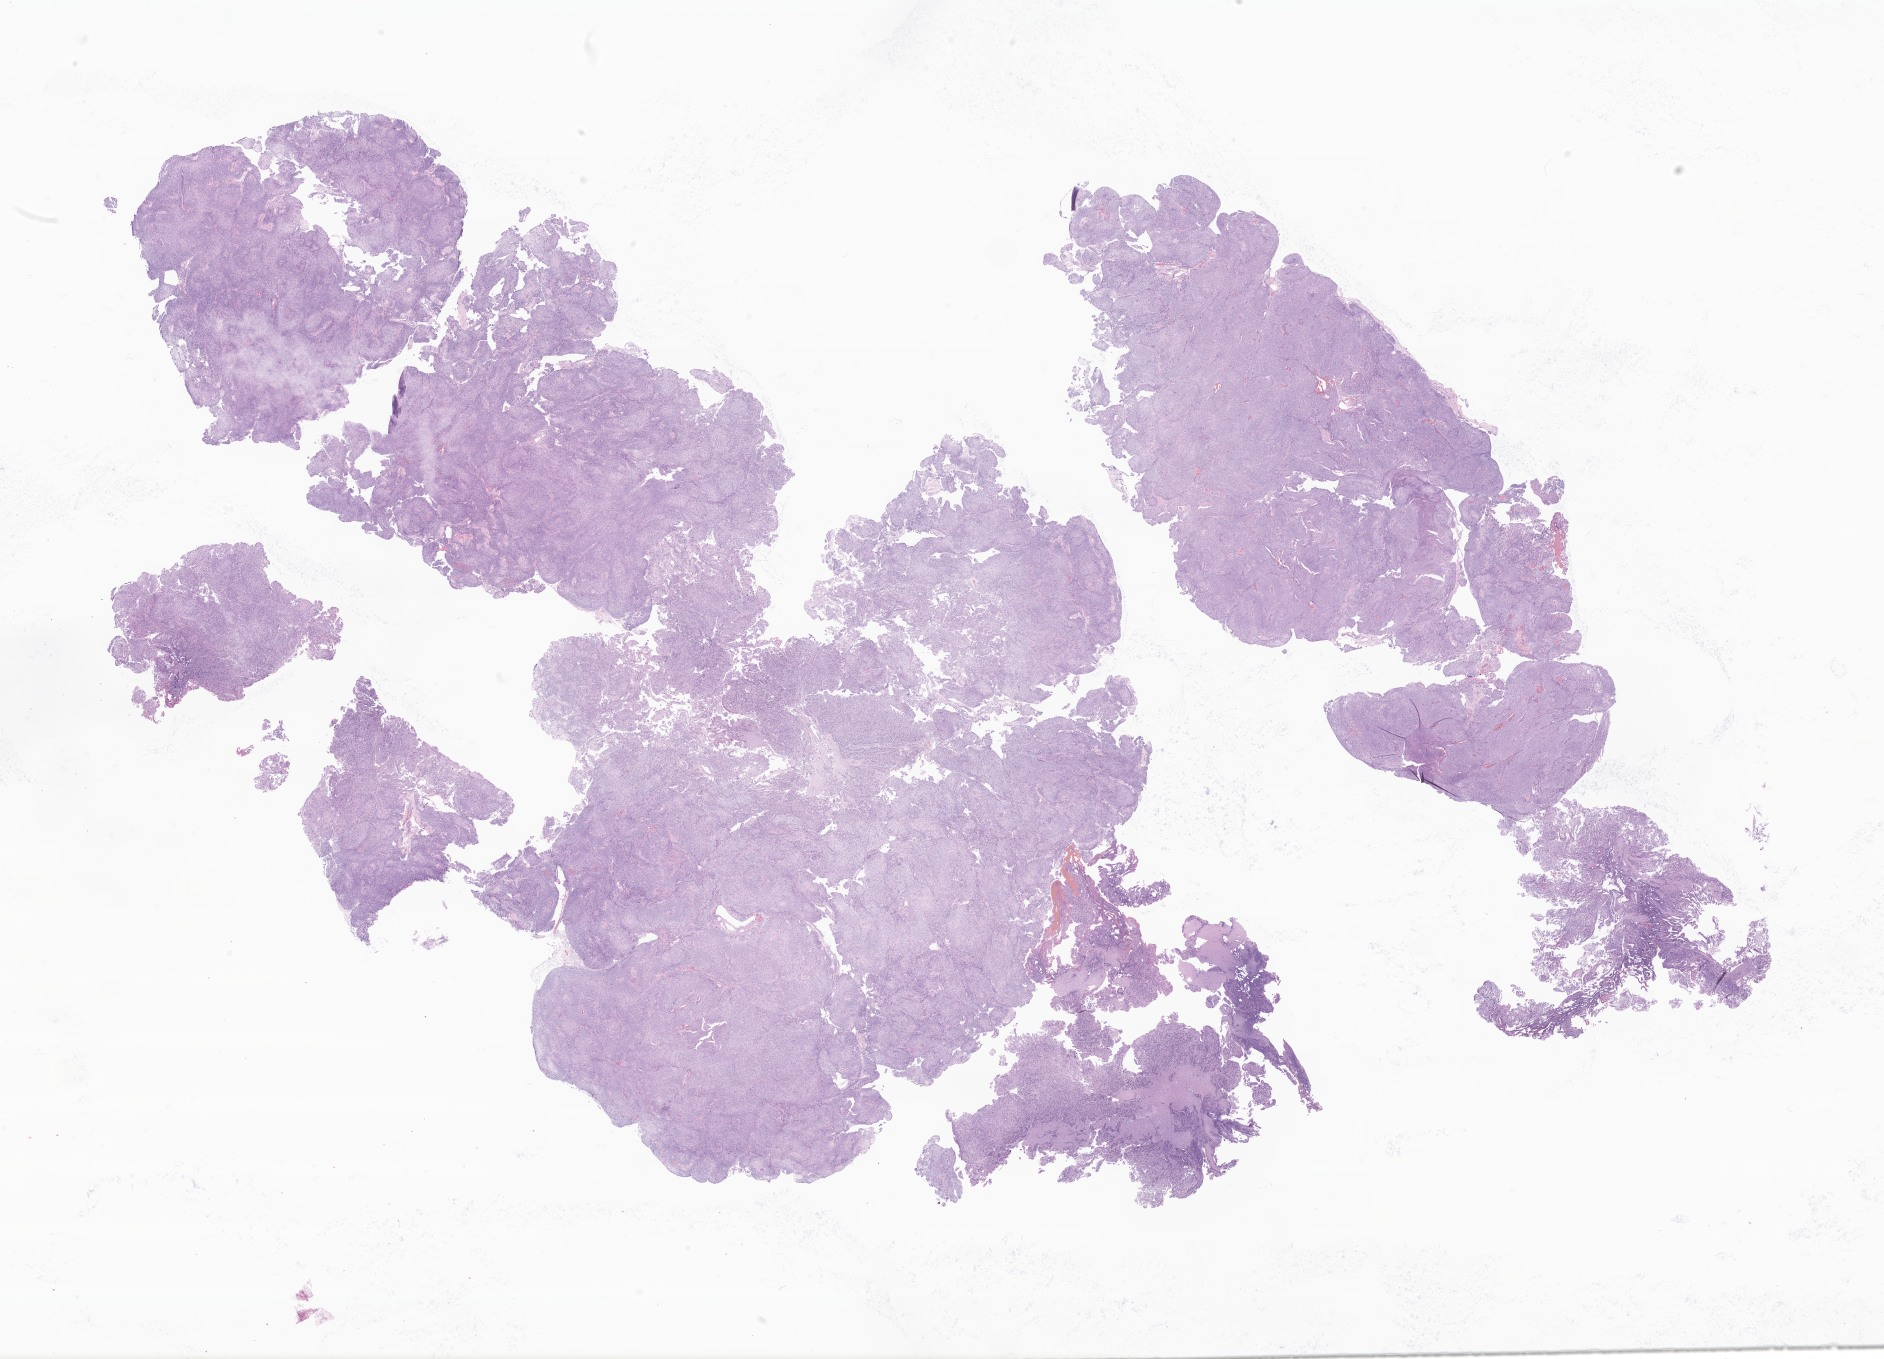
Digitized hematoxylin and eosin (H&E)-stained section of tumor tissue from the brain, shown as a low-resolution overview of the whole scanned area (about 31.8 x 22.9 mm); formalin-fixed, paraffin-embedded (FFPE) tissue. Patient female; age 262 months (21 years 10 months).
Diagnosis (ICD-O-3 morphology term): Meningioma, NOS.